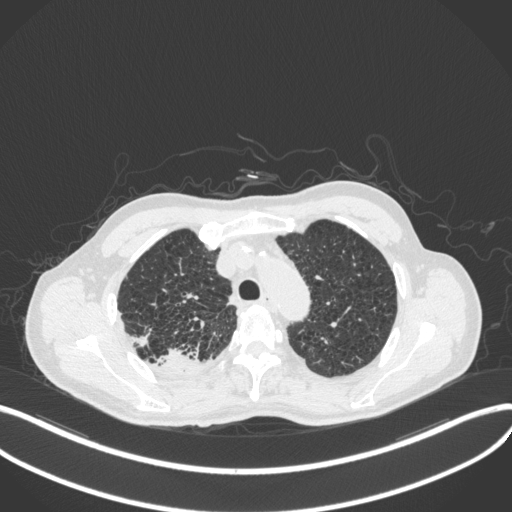
Chest CT, one axial slice. Position 347 of 423 along the scan axis. Lung window (W 1500 / L -600 HU). 1 mm slice thickness. 512 × 512 image matrix. Patient: male, 79 years. From the clinical record (not read from this slice): clinical TNM (as recorded): T3 N0 M0.
Outlined on this slice (rectangle marked by the reading radiologist):
- lung tumour (recorded histology: adenocarcinoma): bounding box <155,345,209,376> (left, top, right, bottom; pixels)